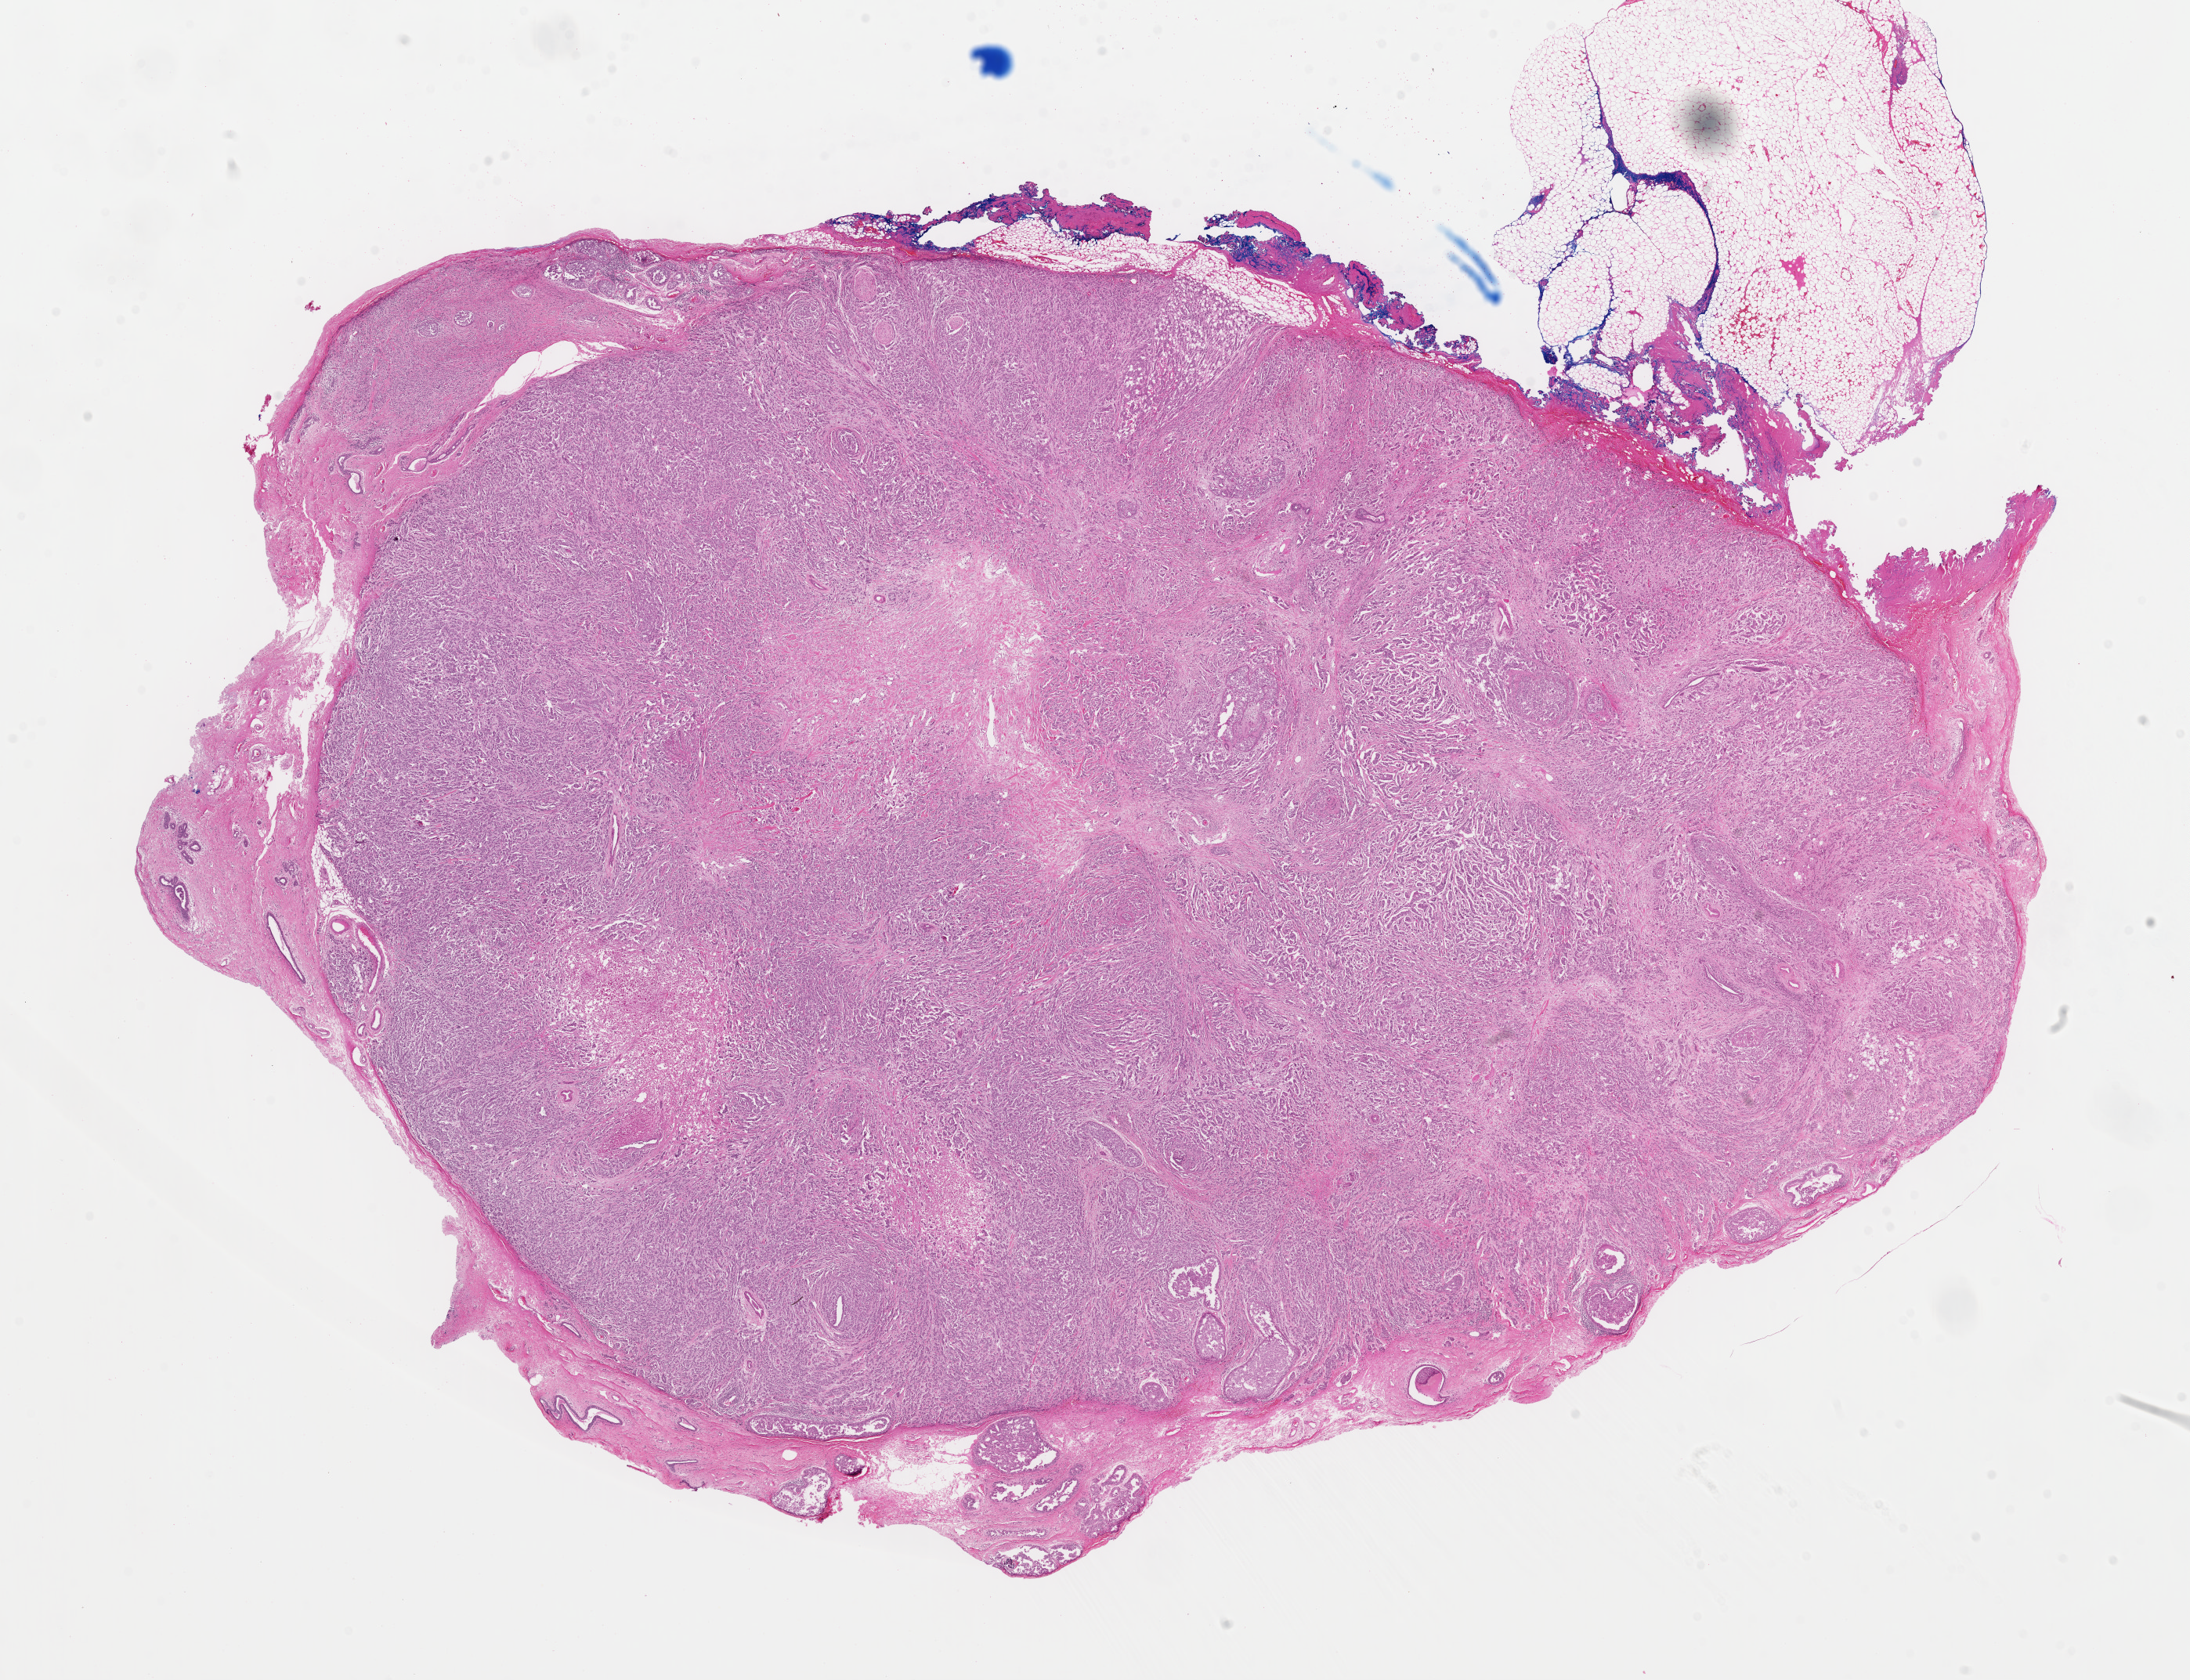
Hematoxylin and eosin (H&E) stained whole-slide image, low-resolution overview of the scanned area, about 22.1 x 16.9 mm. Formalin-fixed paraffin-embedded (FFPE) diagnostic section. Breast, primary tumour sample. Female, age 34 years at initial diagnosis.
Laterality: left. Lymph nodes positive (case pathology): 6 of 10 examined. AJCC pathologic stage: IIIA (6th edition). Pathologic diagnosis: Infiltrating duct carcinoma, NOS.